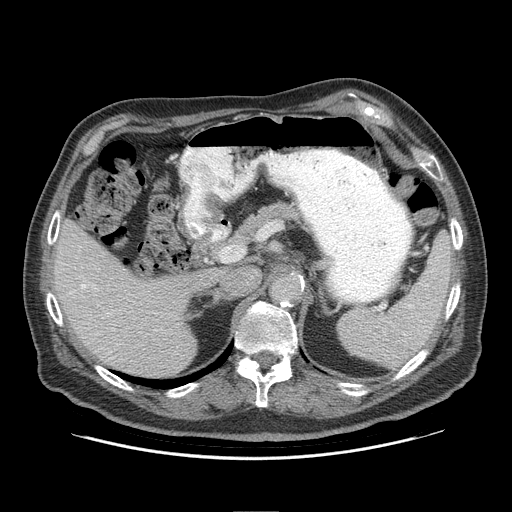
Contrast-enhanced abdominal CT (liver protocol), one axial slice; slice 57 of 95 in the series (ordered by position); reconstruction kernel STANDARD; 140 kVp; soft-tissue window (W 400 / L 40 HU); 512 × 512 image matrix, field of view 400 × 400 mm. Case-level facts recorded for this patient, not image findings: diagnosis: hepatocellular carcinoma (patient treated with transarterial chemoembolisation; whether this scan precedes or follows treatment is not stated here); TNM stage (as recorded): Stage-IVB; Child-Pugh class: A; tumour differentiation: well differentiated; tumour nodularity: uninodular.
Outlined on this slice (semi-automatic segmentation, software-assisted and operator-edited):
- liver parenchyma outside the tumour (the mass and vessels are separate outlines, so this box may not span the whole liver): bounding box [x1, y1, x2, y2] px = [54, 220, 214, 376]
- liver vessels: [81, 284, 114, 329]